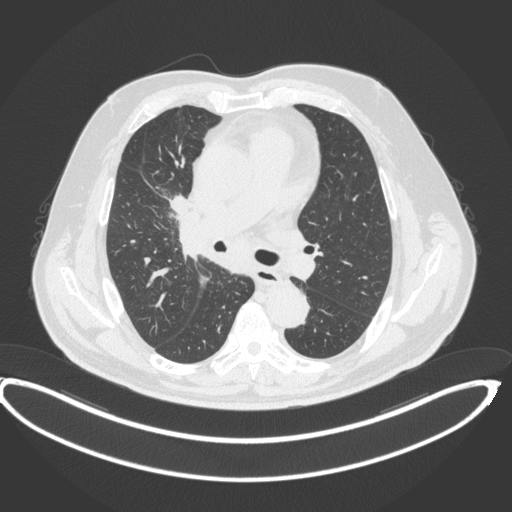
Chest CT, one axial slice. Slice 244 of 395 in the series (ordered by position). 120 kVp. Lung window (W 1500 / L -600 HU). 1 mm slice thickness. 512 × 512 image matrix, field of view 448 × 448 mm. Patient: male, 62 years. From the clinical record (not read from this slice): clinical TNM (as recorded): T1c N3 M1c.
Annotated regions visible in this slice (bounding box drawn by a radiologist):
- lung tumour (recorded histology: adenocarcinoma): bounding box [x1, y1, x2, y2] px = [167, 190, 192, 214]